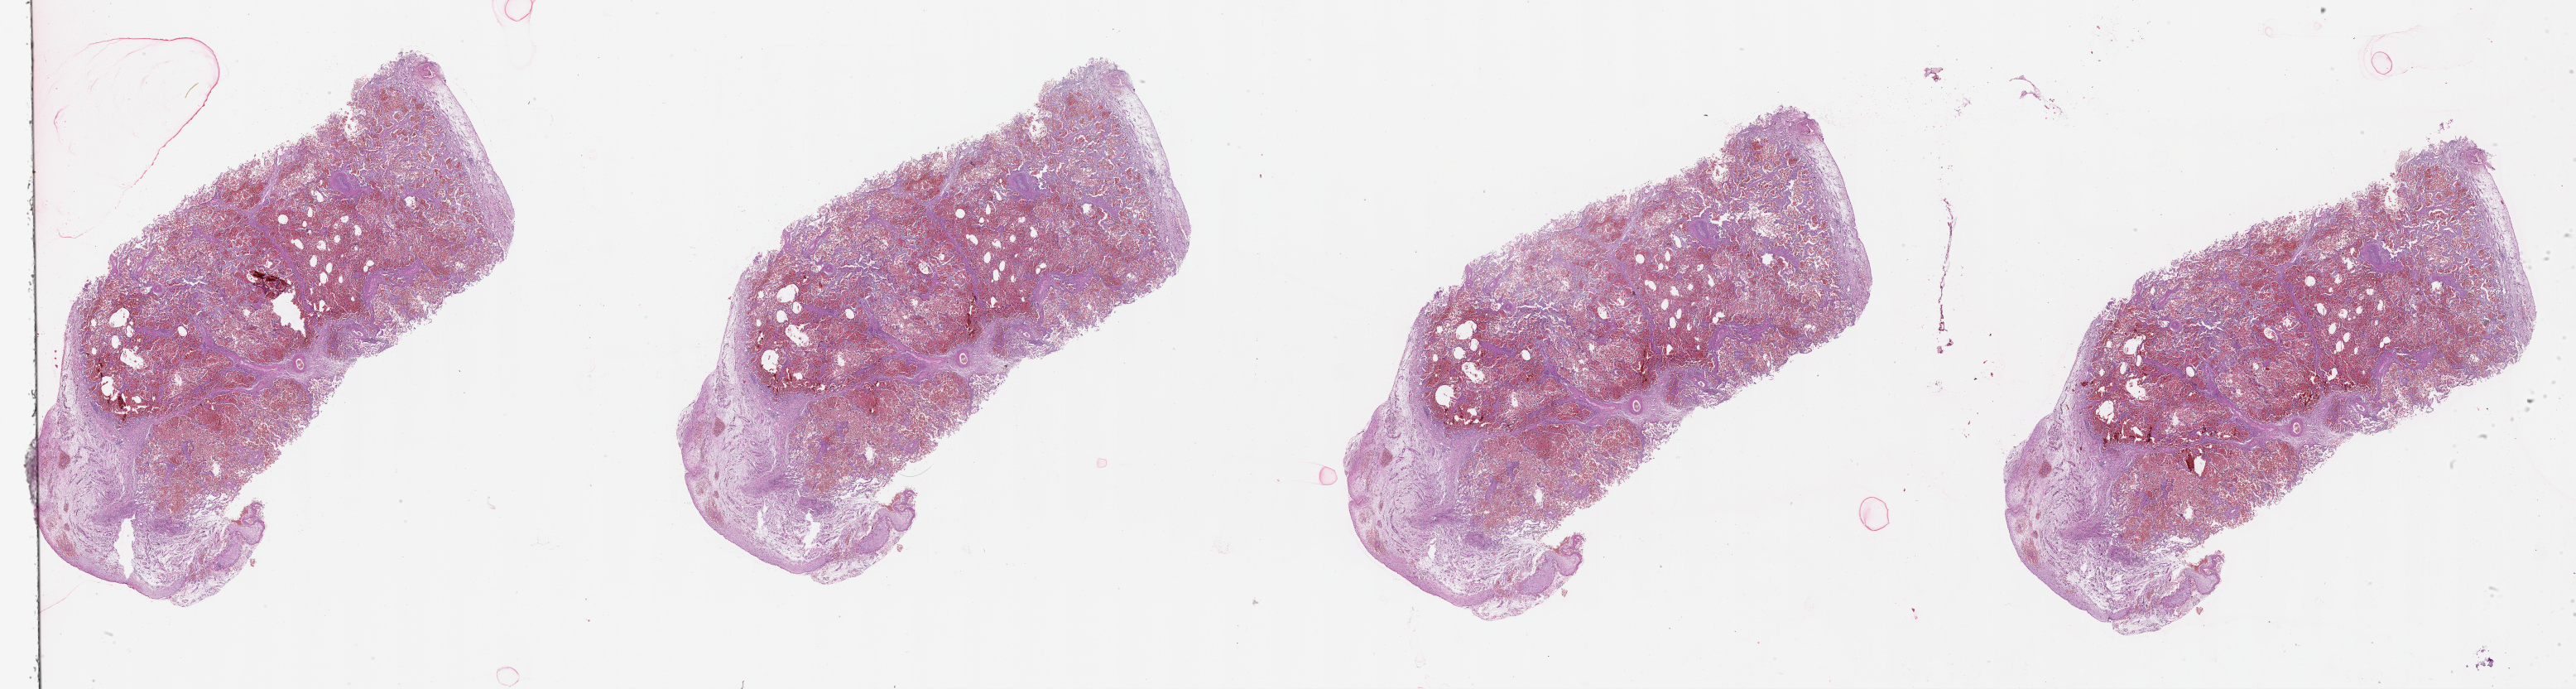
Digitized Hematoxylin and eosin (H&E) stained tissue section (whole slide), shown as a low-resolution overview of the whole scanned area (about 50.1 x 13.4 mm, acquisition: 20x scan). Normal (non-tumour) tissue sample, lung. 74-year-old male patient.
- this section: normal (non-tumour) tissue from the same patient
- patient diagnosis (cohort enrolment): squamous cell carcinoma (lung)